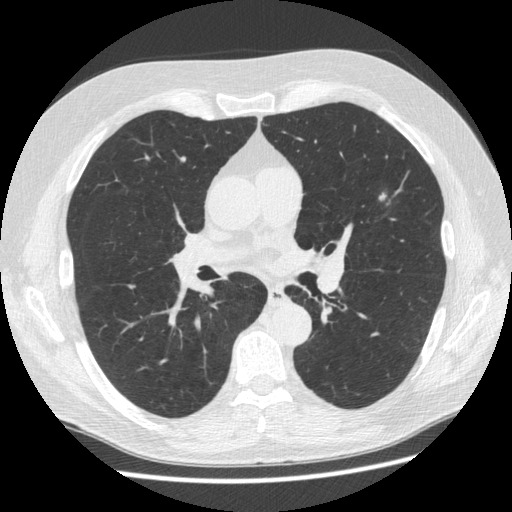
Low-dose screening chest CT, one axial slice. Position 304 of 545 along the scan axis. 120 kVp. Lung window (W 1500 / L -600 HU). 512 × 512 image matrix, field of view 360 × 360 mm.
Outlined on this slice (expert manual segmentation):
- lesion 1 (nodule, upper lobe of left lung): bounding box <379,191,387,201> (left, top, right, bottom; pixels)